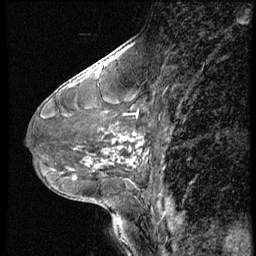
Breast MRI (dynamic contrast-enhanced), one sagittal slice. Slice 25 of 56 in the series (ordered by position). Dynamic contrast-enhanced series, image 2 of 3 at this slice position (ordered by acquisition). 1.5 T. TE 4.2 ms, TR 9 ms. 256 × 256 image matrix, field of view 180 × 180 mm. Female patient, age 46 years. Case-level facts recorded for this patient, not image findings: setting: breast cancer imaged before/during neoadjuvant chemotherapy; receptor status: HER2-positive.
Structures marked on this image (semi-automatically segmented with operator editing):
- analysis volume of interest (the breast-tissue region the enhancement analysis was run in; not a lesion): bounding box <64,98,174,182> (left, top, right, bottom; pixels)
- tumour enhancement mask (voxels above the 140 % enhancement threshold inside the analysis volume of interest): <75,133,144,178>